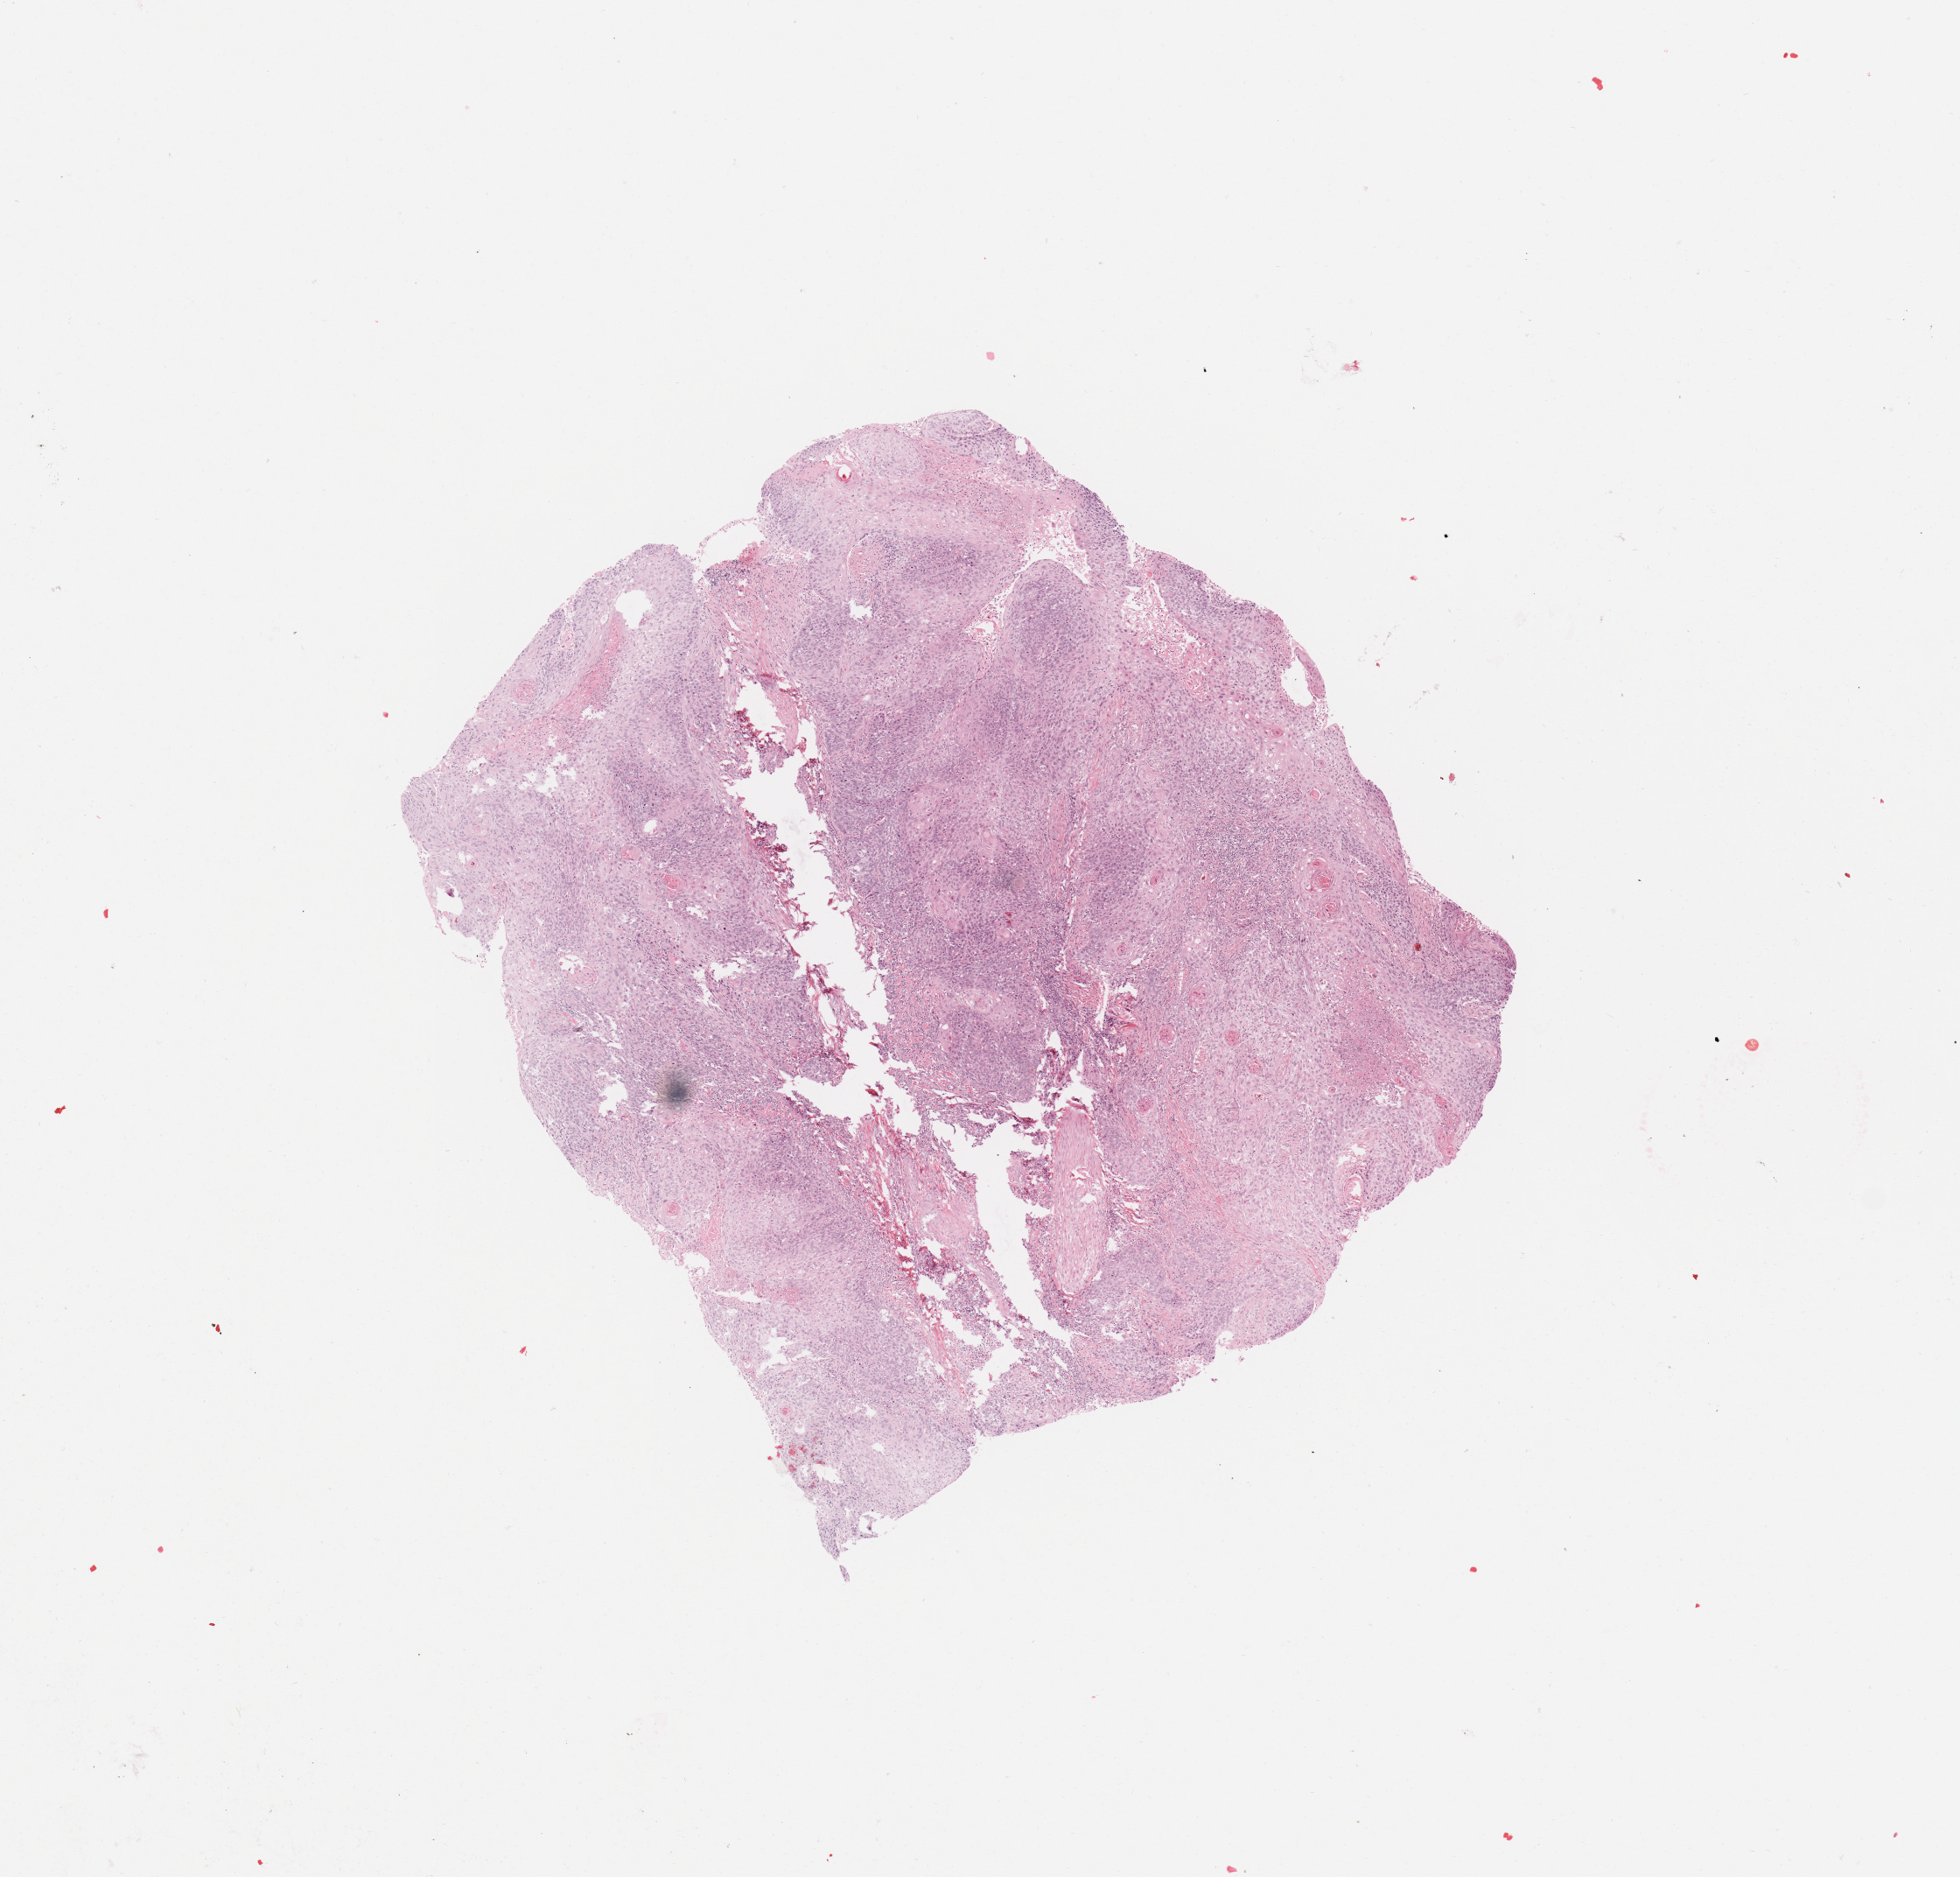
Whole-slide histology image, H&E-stained — shown as a low-resolution overview of the whole scanned area (about 8.9 x 8.5 mm, slide scanned at 20x), tumour tissue sample, sampled site: larynx. Male, 52 y/o. Histologic grade: G1 (well differentiated). Slide review estimates, as recorded: tumour nuclei 80%, necrosis 5%.
Diagnosis: Squamous cell carcinoma, NOS. AJCC pathologic stage: III.